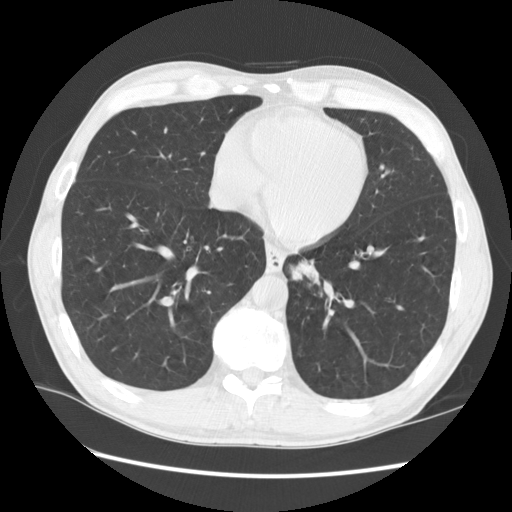
Low-dose screening chest CT, one axial slice; position 44 of 141 along the scan axis; reconstruction kernel STANDARD; 120 kVp; lung window (W 1500 / L -600 HU); 2.5 mm slice thickness; 512 × 512 image matrix.
Annotated regions visible in this slice (manually delineated by an expert):
- lesion 2 (nodule, lower lobe of left lung): bounding box (x1, y1, x2, y2) in pixels: (291, 259, 319, 282)